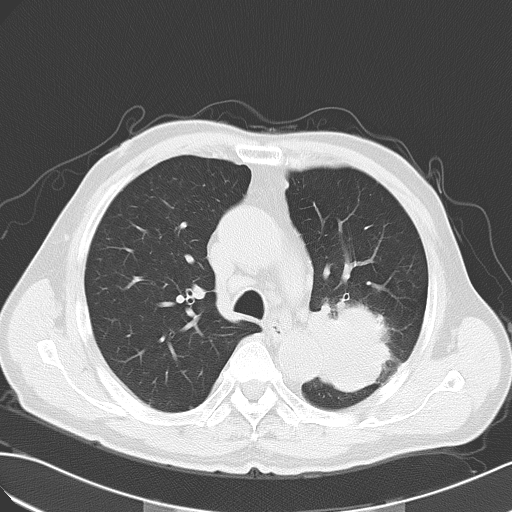
Chest CT, one axial slice. Slice 38 of 55 in the series (ordered by position). Reconstruction kernel B70f. Lung window (W 1500 / L -600 HU). 512 × 512 image matrix. Male patient, age 63 years. From the clinical record (not read from this slice): clinical TNM (as recorded): T3 N3 M1a.
Outlined on this slice (bounding box drawn by a radiologist):
- lung tumour (recorded histology: large cell carcinoma): bounding box <307,300,390,397> (left, top, right, bottom; pixels)